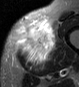
MRI of an extremity soft-tissue mass, one axial slice. STIR. MR volume resampled by the dataset authors to the PET/CT grid (not the native acquisition matrix). 3.27 mm slice thickness. 79 × 87 image matrix. Male patient. From the clinical record (not read from this slice): histological type: pleiomorphic leiomyosarcoma; grade: high; site of the primary tumour: left thigh.
Annotated regions visible in this slice (expert contour drawn on MRI and transferred to this co-registered scan by the dataset authors):
- gross tumour volume including surrounding oedema: box from (x=15, y=20) to (x=58, y=69) px
- gross tumour volume (mass): (x=15, y=20)–(x=55, y=62)